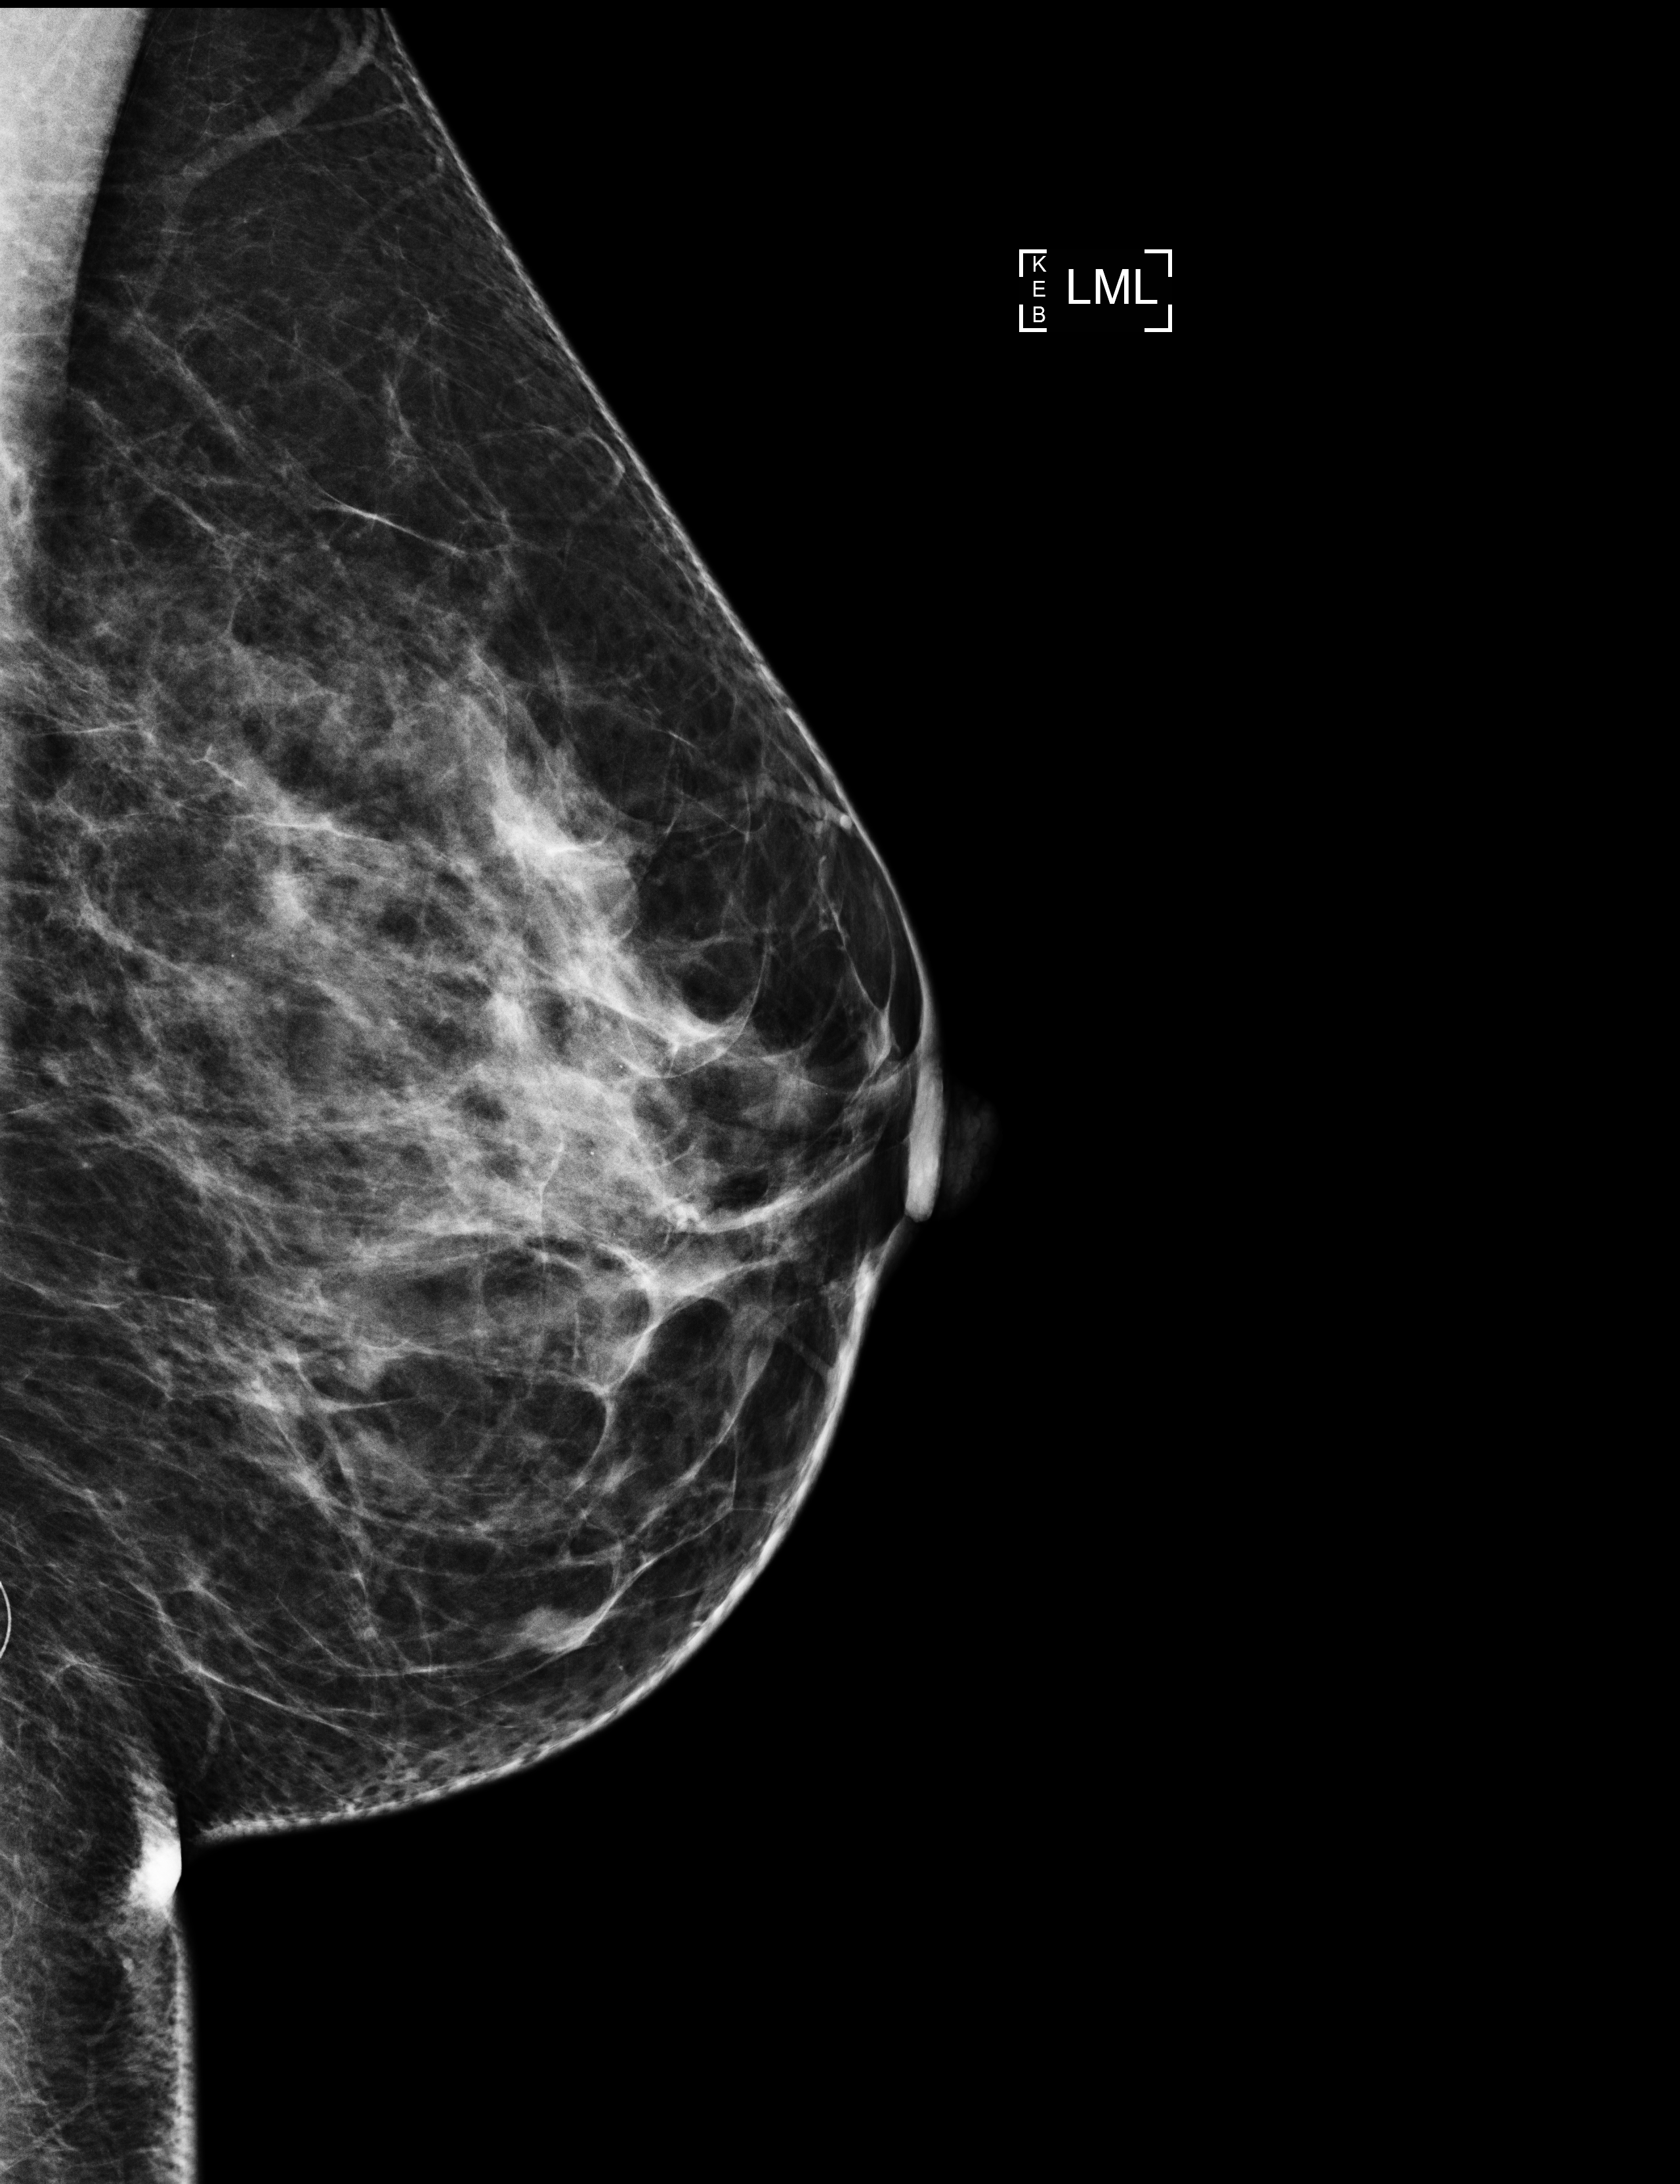
Digital mammogram (FFDM), left breast, mediolateral (ML) view, diagnostic examination (additional views). Female patient, age 41 years.
BI-RADS breast density category at the screening exam (both breasts, scale 1–4): 3. Final BI-RADS category for the screening round (tomosynthesis exam, both breasts): category 3. Recall: recalled for additional imaging after this screen.